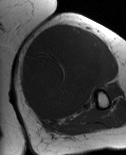
MRI of an extremity soft-tissue mass, one axial slice. Slice 42 of 86 in the series (ordered by position). MR volume resampled by the dataset authors to the PET/CT grid (not the native acquisition matrix). 126 × 155 image matrix, field of view 123 × 151 mm. Female patient. Case-level facts recorded for this patient, not image findings: histological type: pleiomorphic leiomyosarcoma; grade: high; site of the primary tumour: left biceps.
Annotated regions visible in this slice (expert contour drawn on MRI and transferred to this co-registered scan by the dataset authors):
- gross tumour volume including surrounding oedema: bounding box (x1, y1, x2, y2) in pixels: (20, 26, 108, 121)
- gross tumour volume (mass): (20, 26, 107, 119)